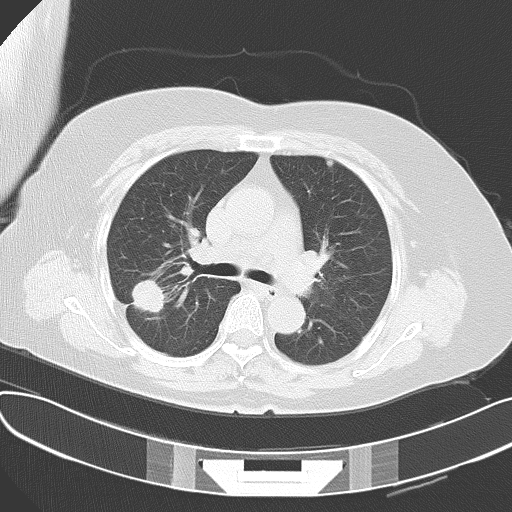
Chest CT, one axial slice; position 44 of 61 along the scan axis; lung window (W 1500 / L -600 HU); 5 mm slice thickness; 512 × 512 image matrix. Female patient, age 63 years. From the clinical record (not read from this slice): clinical TNM (as recorded): T1c N3 M1a.
Outlined on this slice (rectangle marked by the reading radiologist):
- lung tumour (recorded histology: adenocarcinoma): bounding box (x1, y1, x2, y2) in pixels: (128, 275, 172, 330)